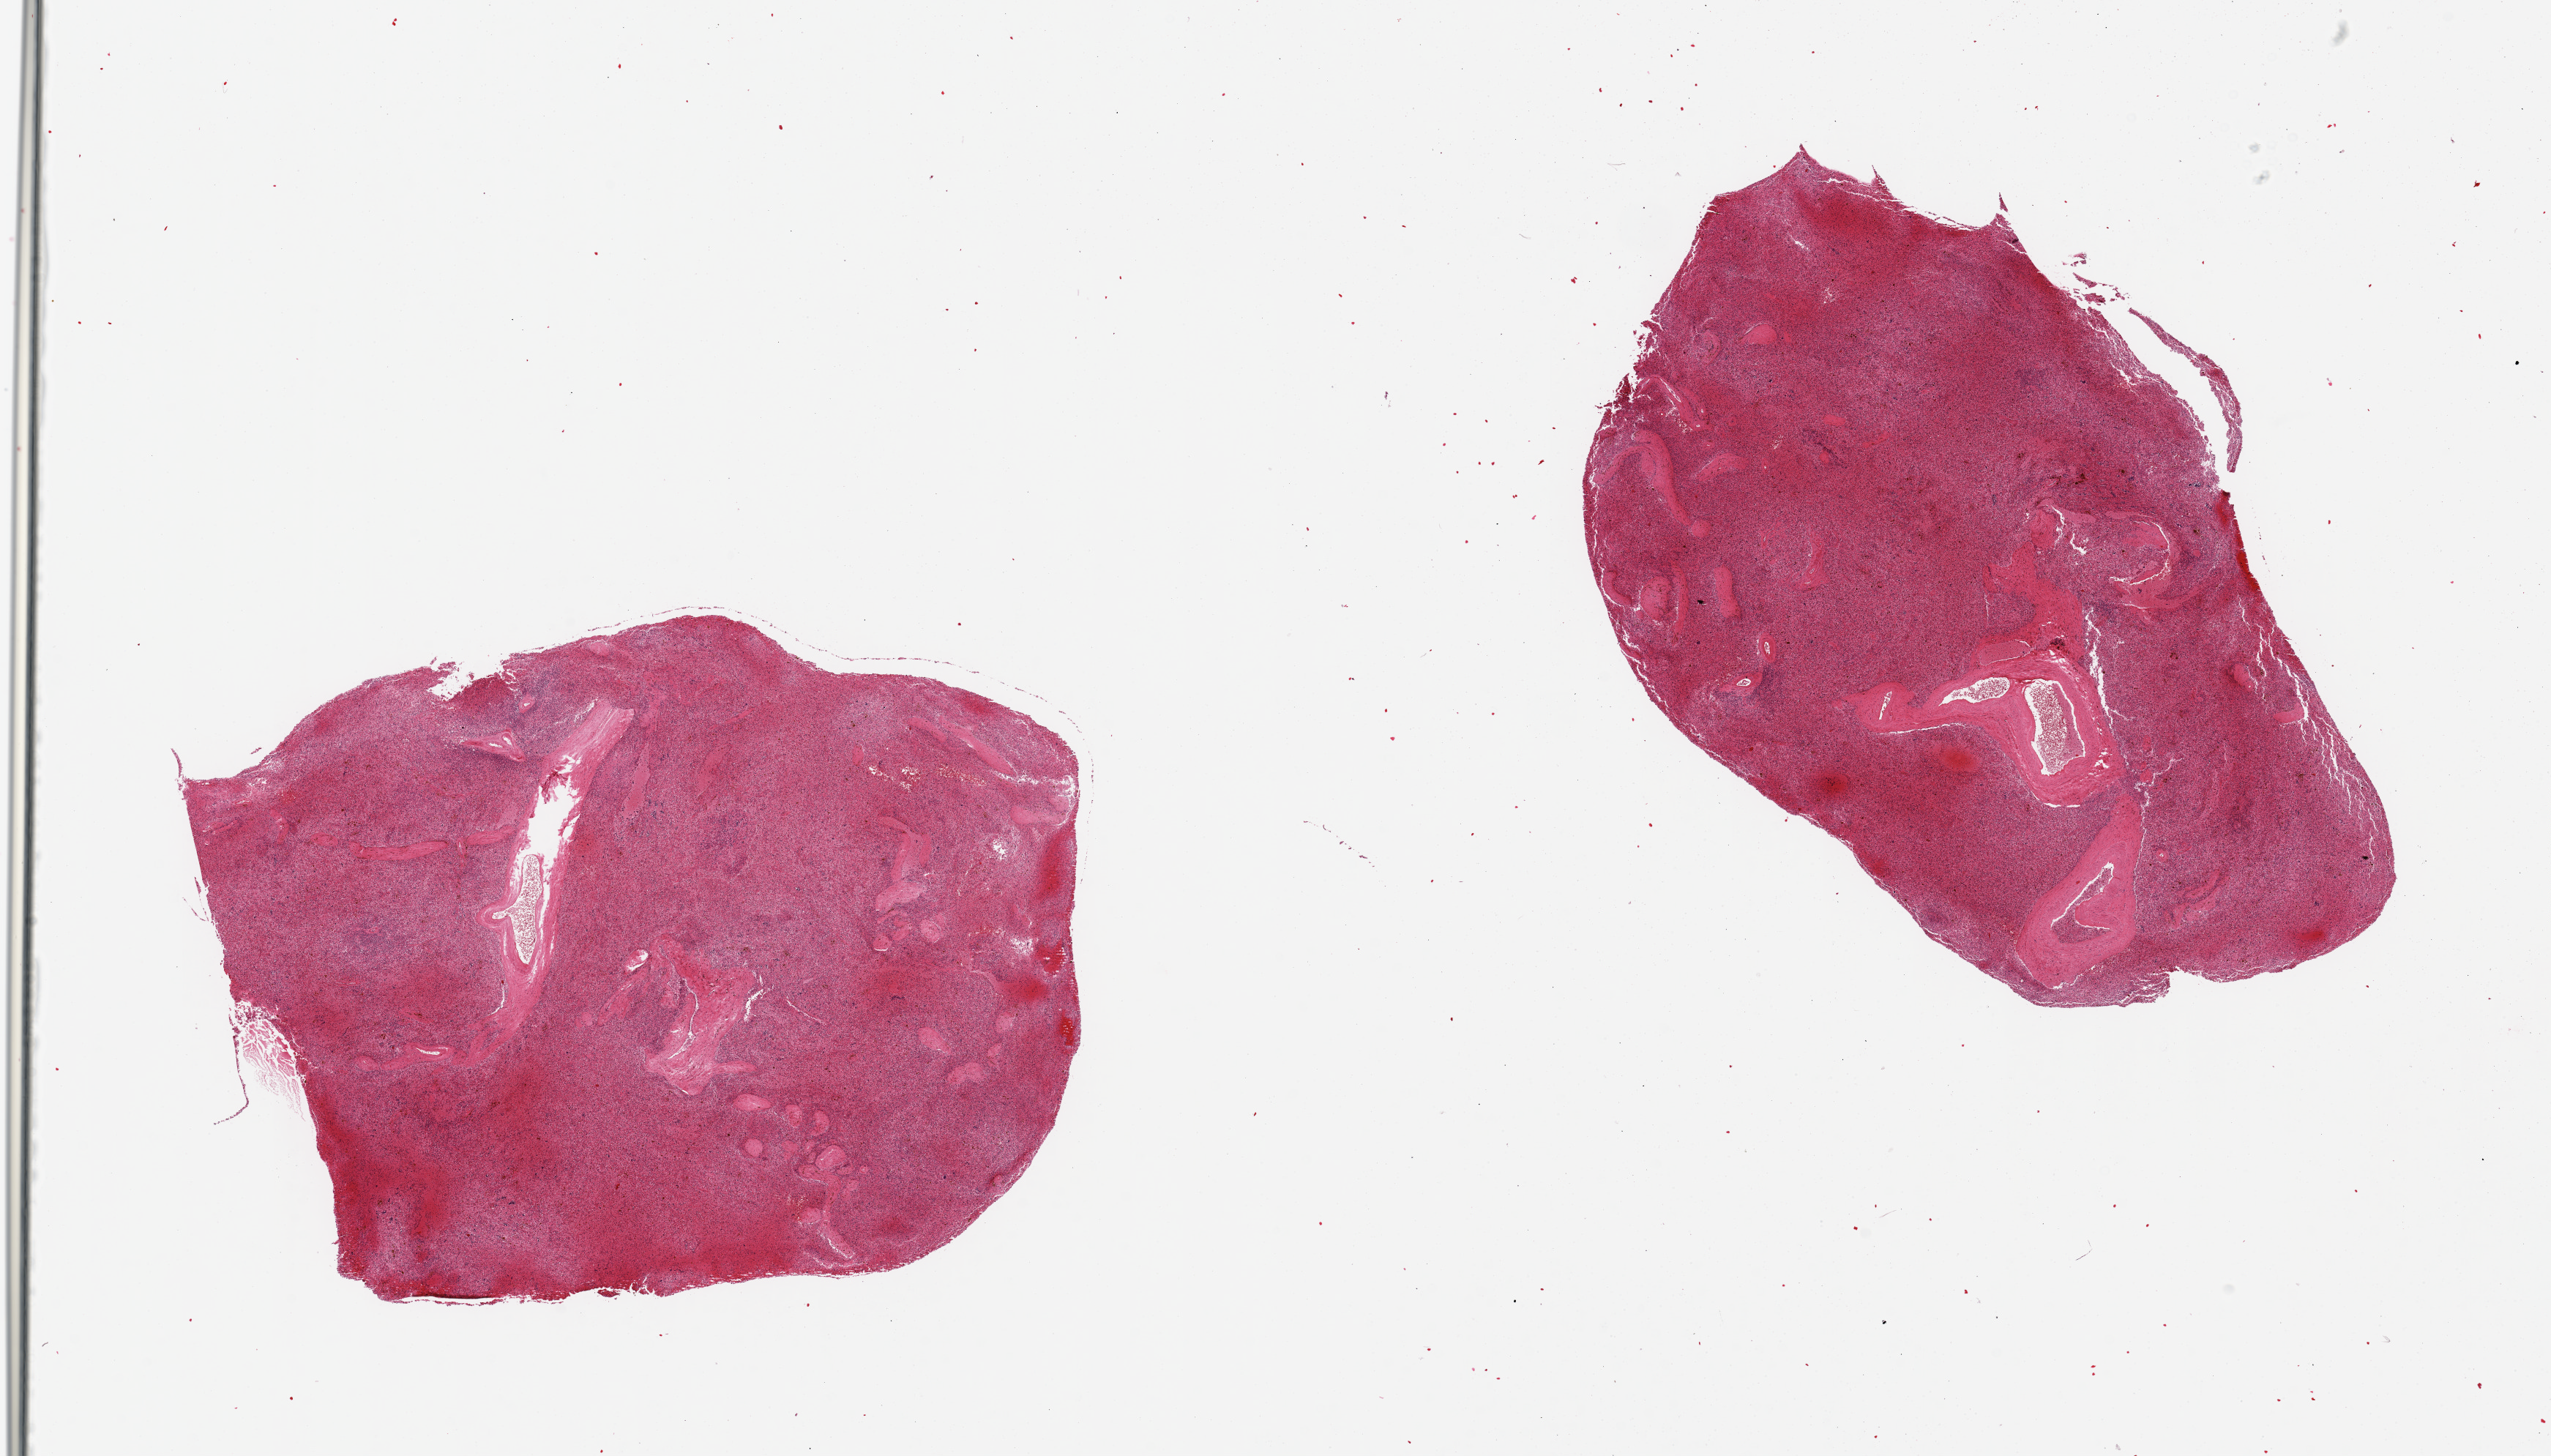
Hematoxylin and eosin (H&E) whole-slide image, shown as a low-resolution overview of the whole scanned area (about 27.6 x 15.7 mm); PAXgene-fixed, paraffin-embedded tissue; target tissue: spleen; tissue donor sample. Female donor.
Review note (as recorded): 2 pieces, congested.